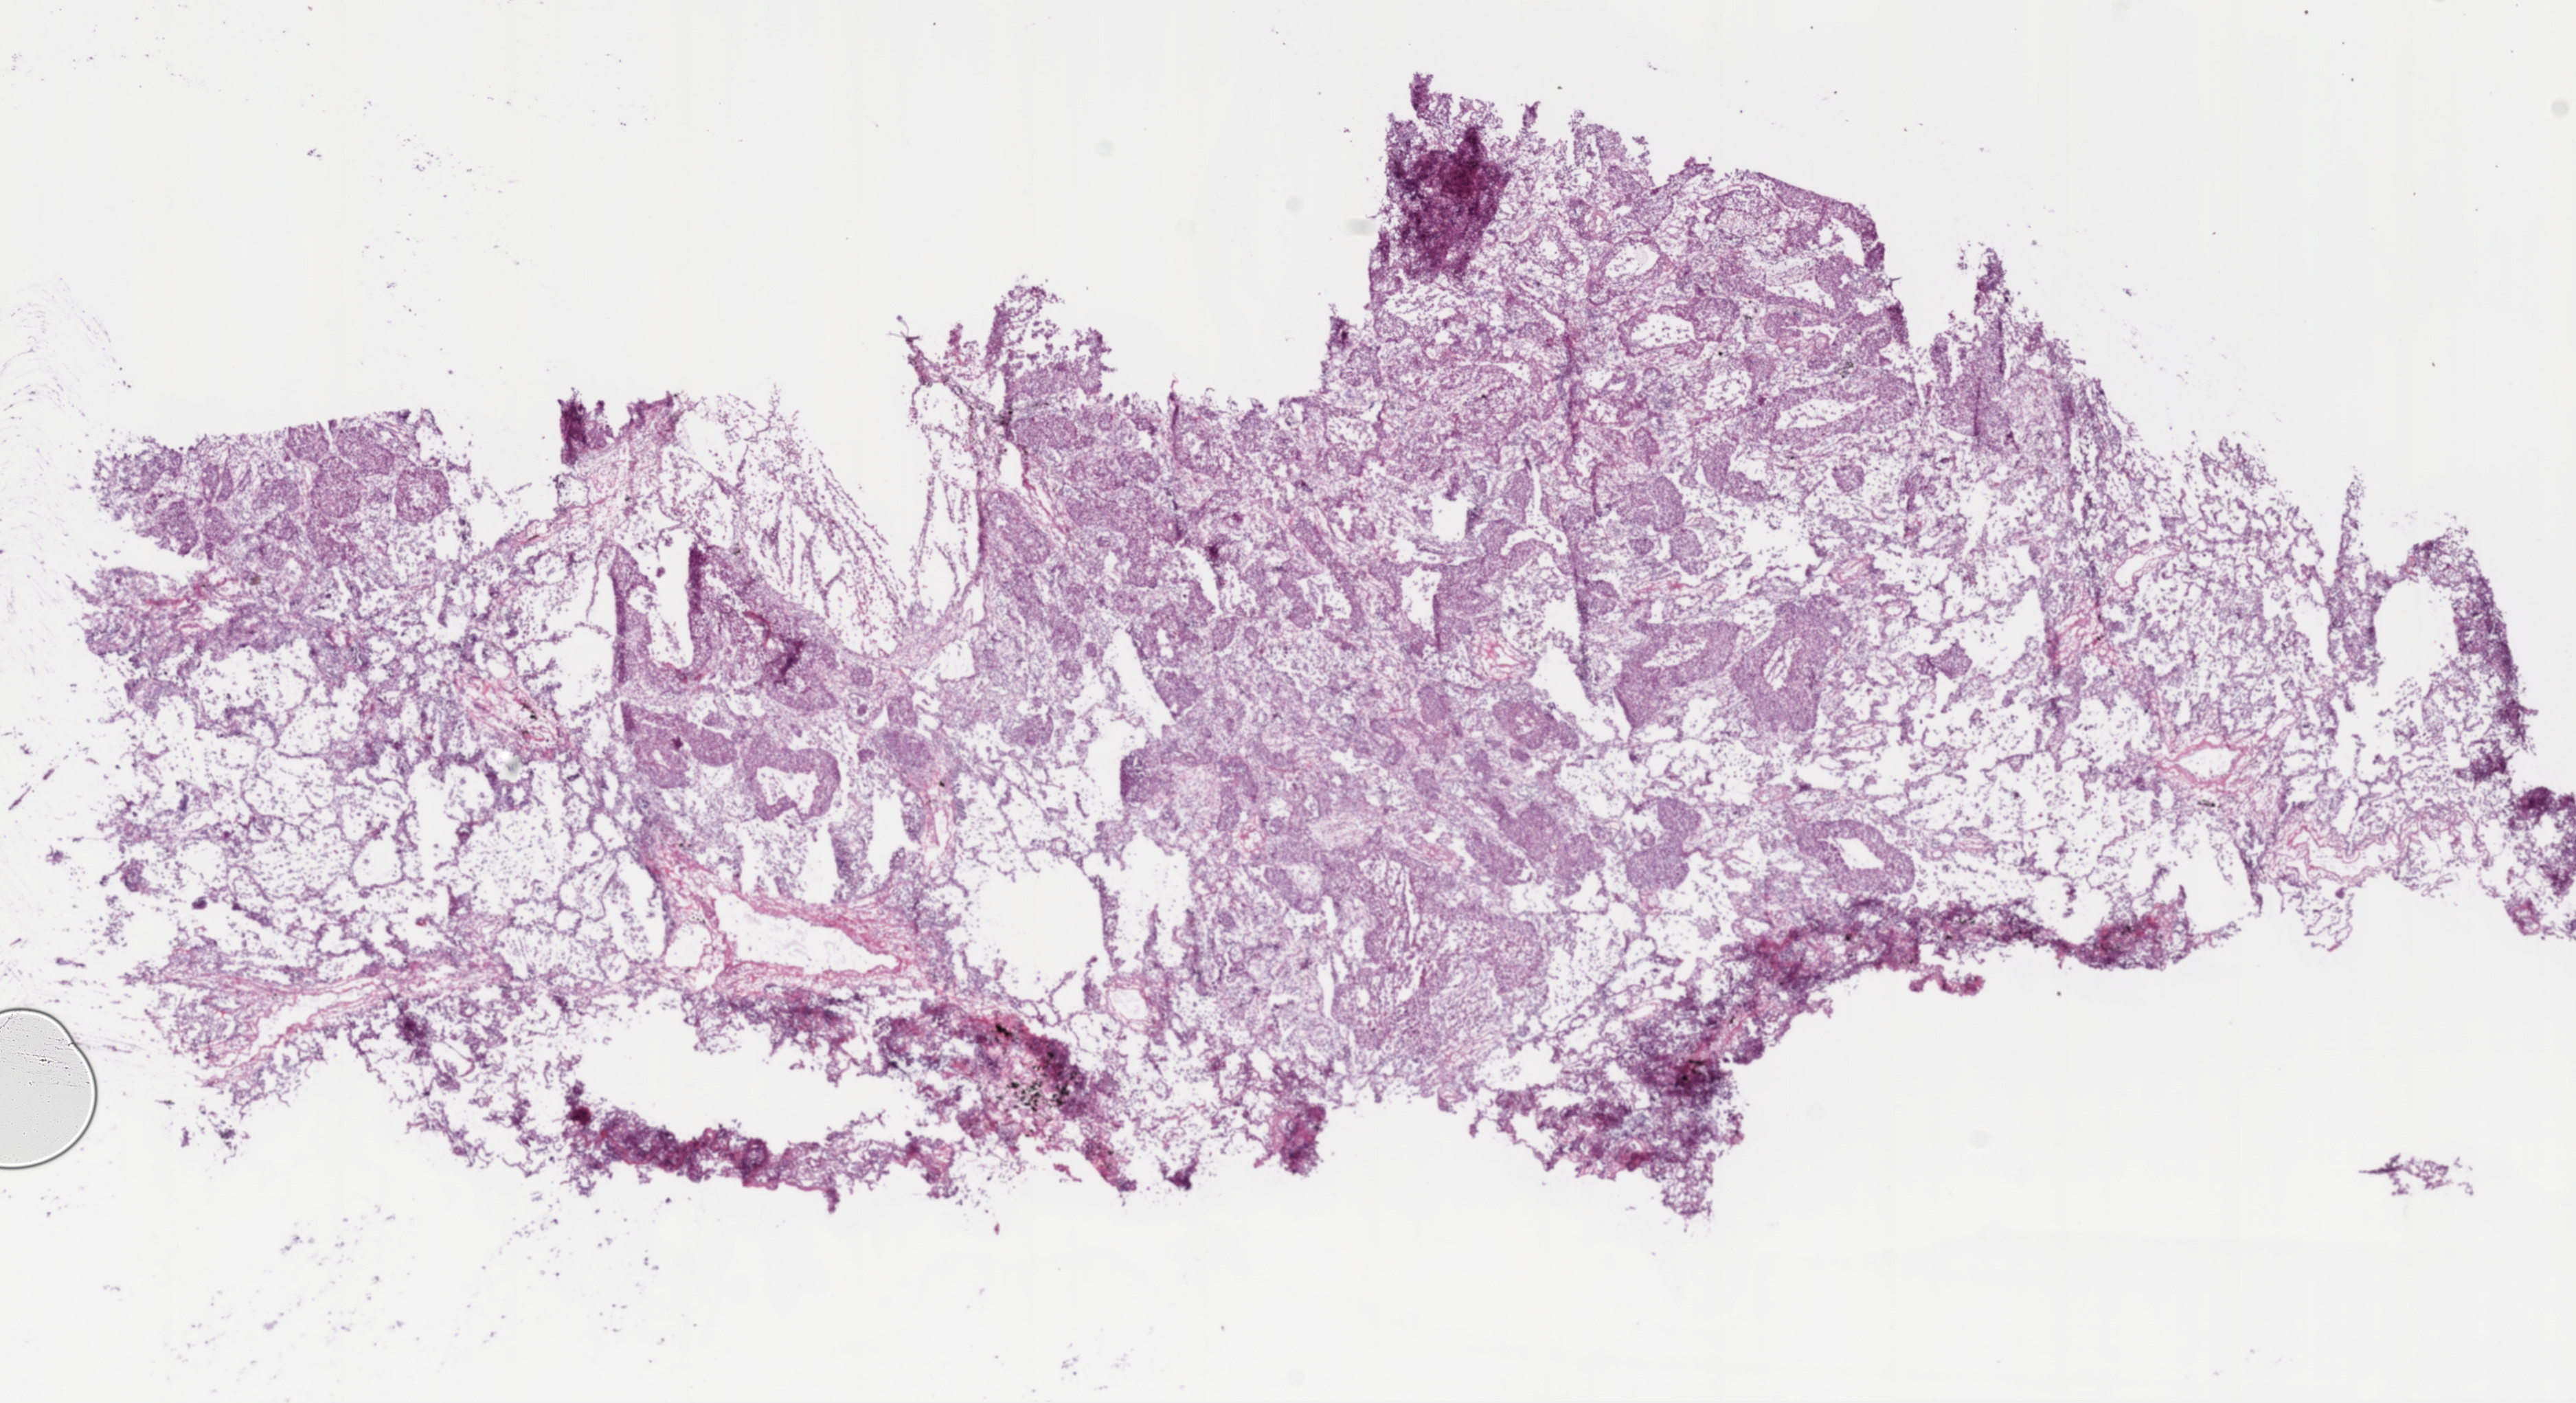
H&E-stained whole-slide image, whole scanned area (about 15.0 x 8.2 mm, acquisition: 20x scan) shown as a low-resolution overview, frozen section from the top of the tissue portion, sample: primary tumour, lung. Female, age 81 years at initial diagnosis. Pathologist review of this section (percent, as recorded): tumour cells 75%, tumour nuclei 90%, normal cells 15%, stromal cells 5%, necrosis 5%. Infiltration values recorded for this section: lymphocyte infiltration 3%, monocyte infiltration 1%, neutrophil infiltration 4%.
Pathologic diagnosis: Squamous cell carcinoma, NOS. AJCC pathologic stage: IB.